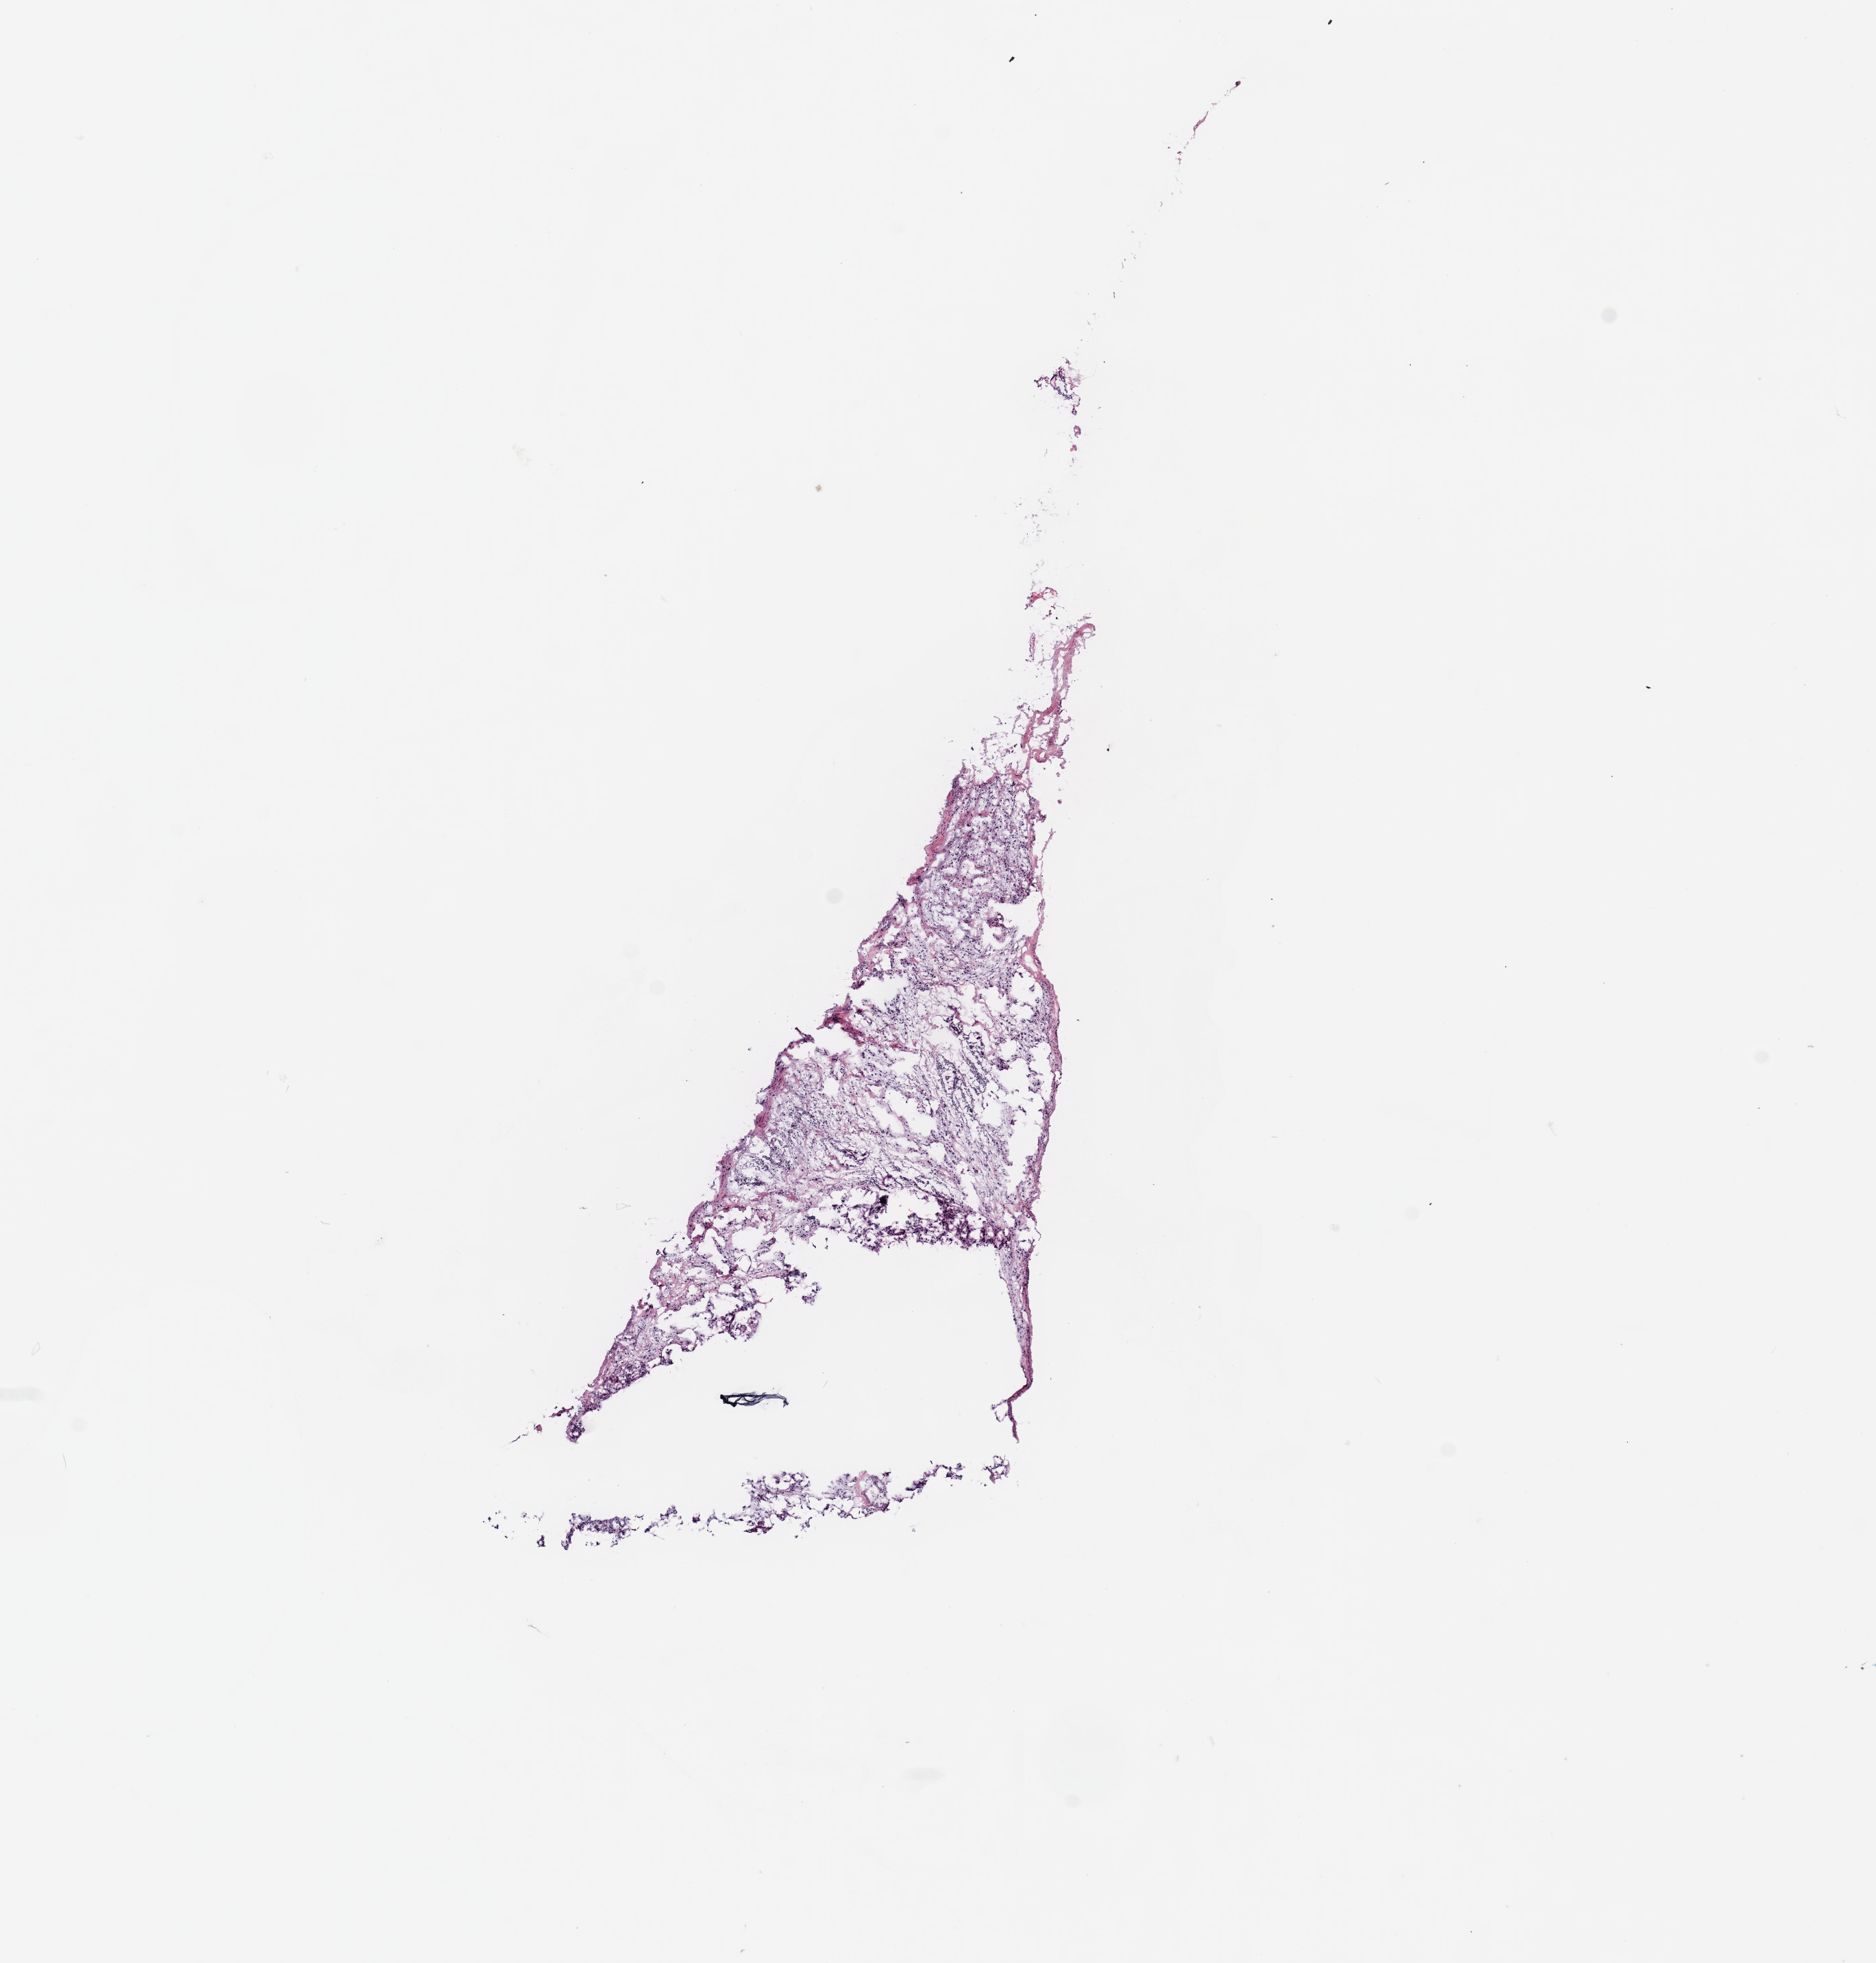
Digitized H&E-stained tissue section (whole slide) — whole scanned area (about 10.8 x 11.3 mm) shown as a low-resolution overview. Breast, tissue type not recorded.
* patient diagnosis (cohort enrolment): breast cancer (breast)